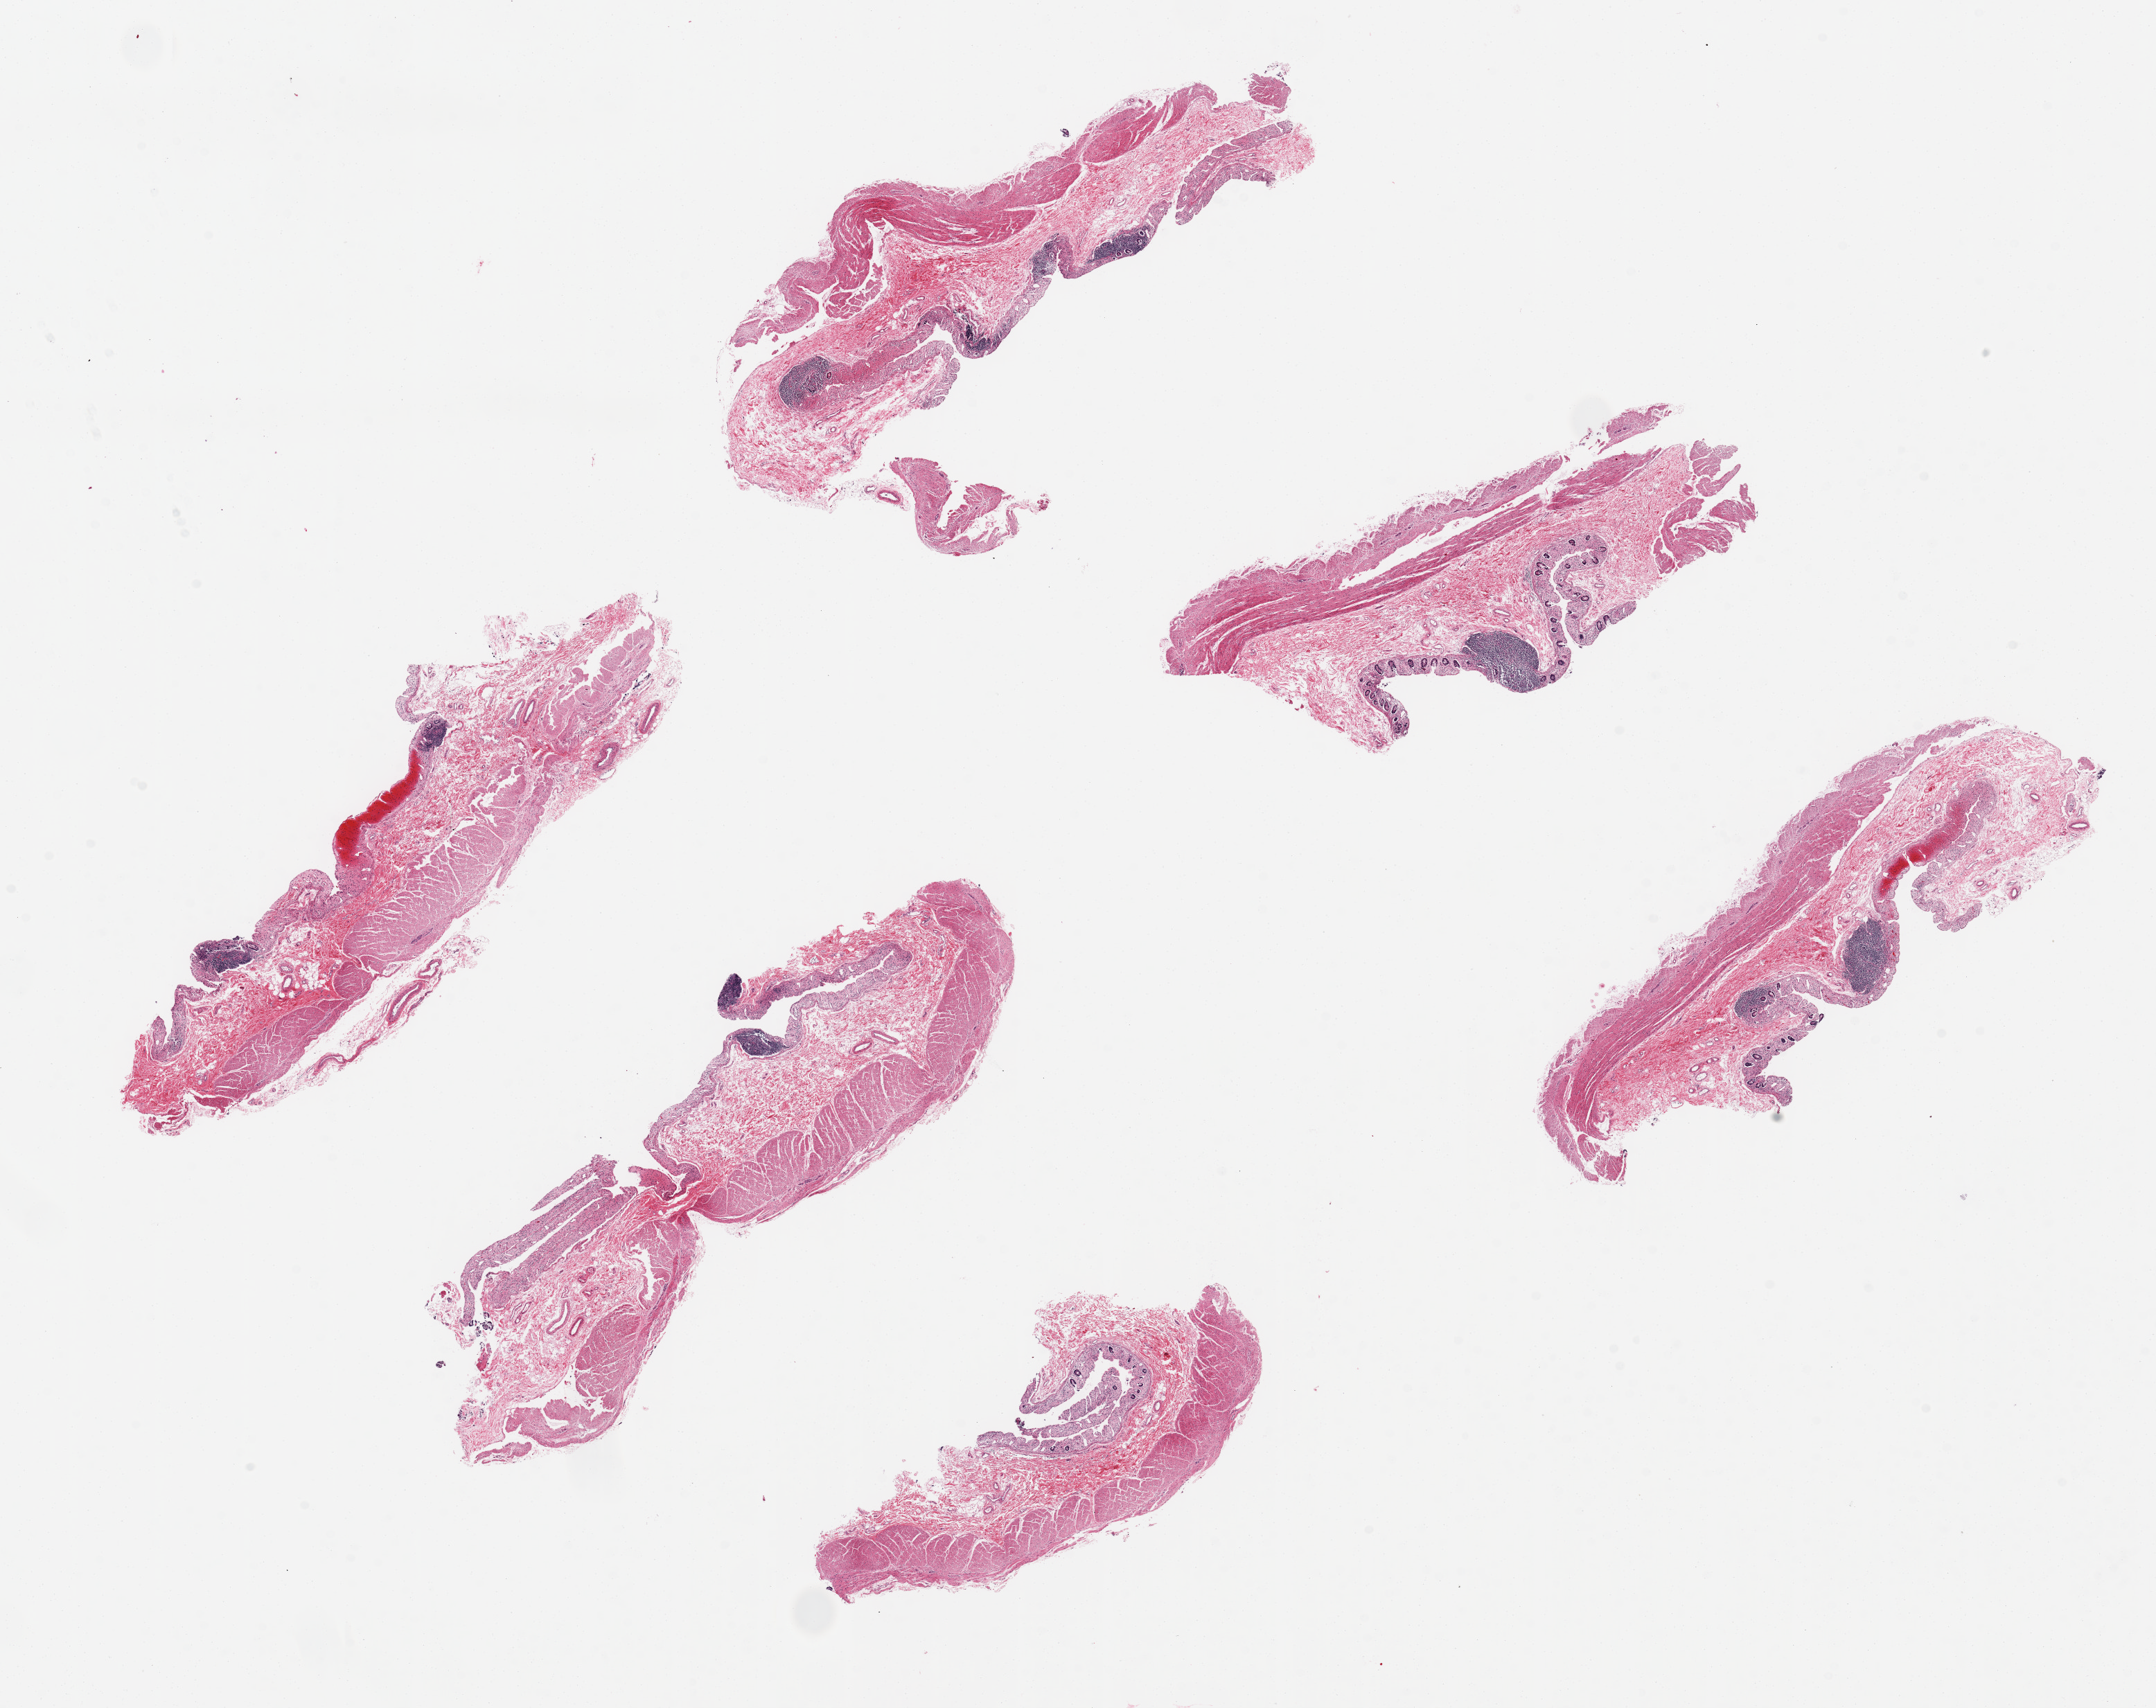
Haematoxylin and eosin whole-slide image, whole scanned area (about 24.6 x 19.5 mm) shown as a low-resolution overview; PAXgene-fixed, paraffin-embedded tissue; target tissue: transverse colon; donor tissue sample. Donor sex: male.
• review note (as recorded): 6 pieces up to 8.7x2.6 mm; mucosa almost completely autolyzed; muscle moderately autolyzed